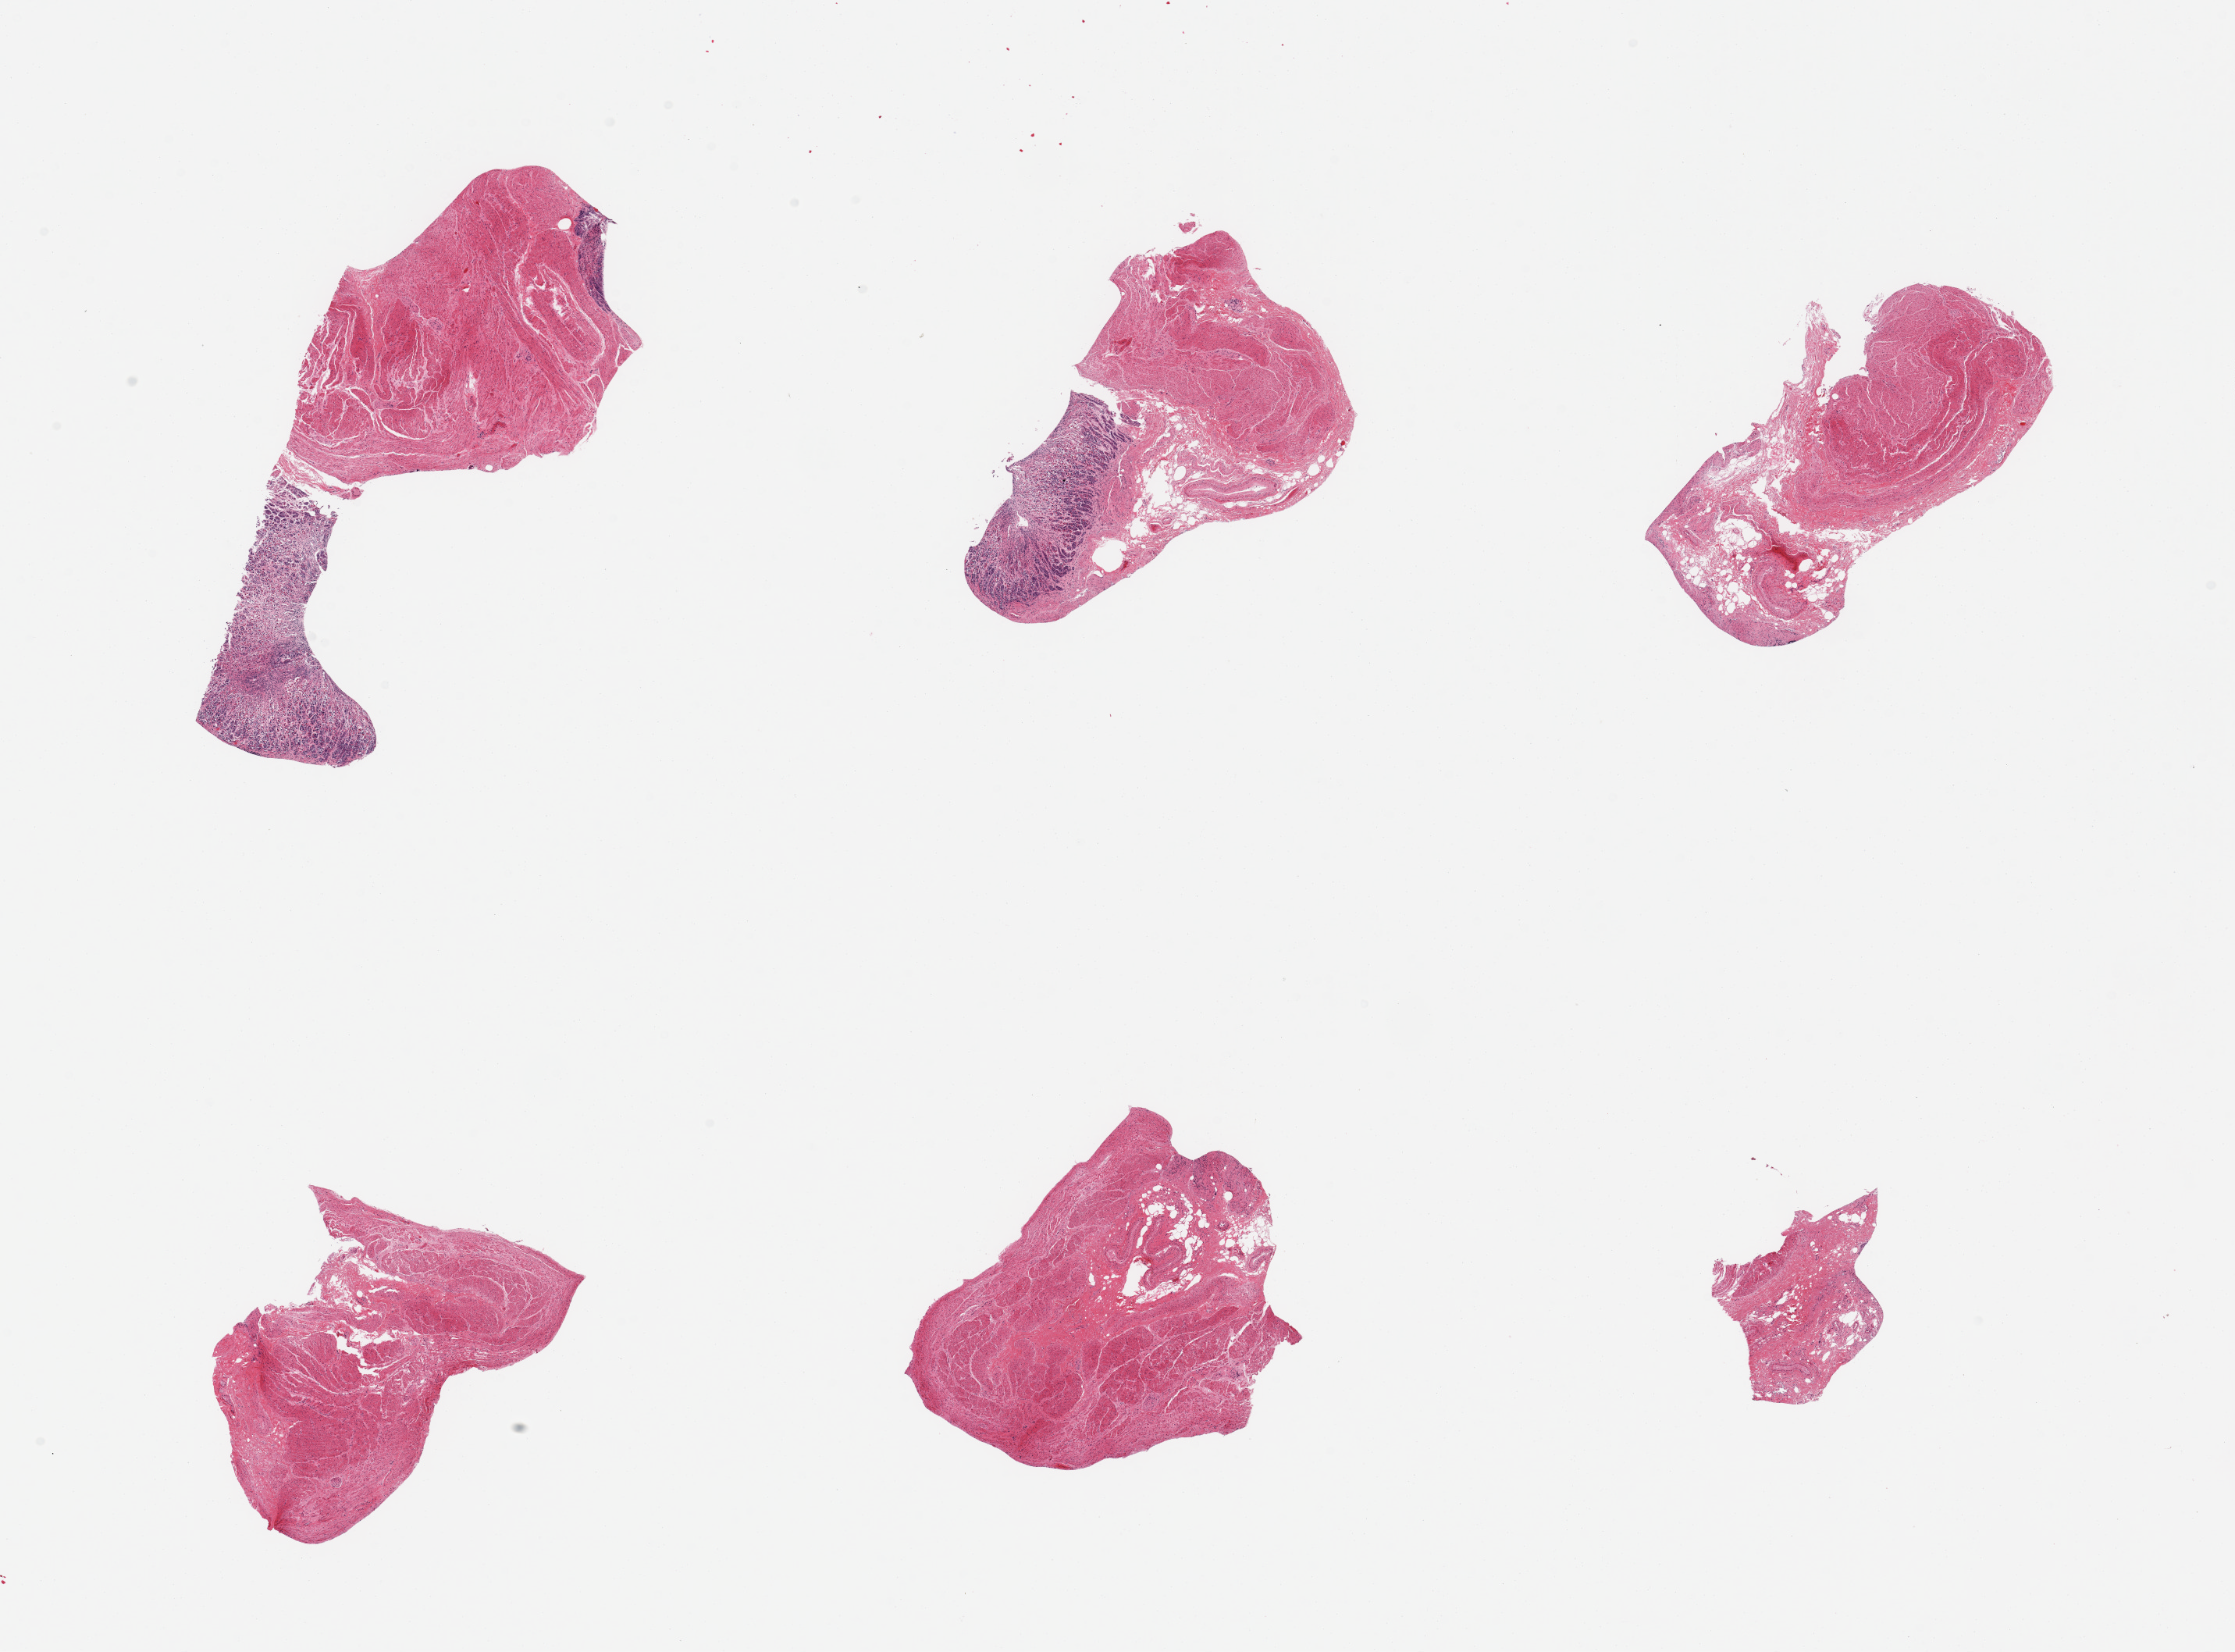
Whole-slide image, hematoxylin and eosin (H&E) stain, brightfield, shown as a low-resolution overview of the whole scanned area (about 22.6 x 16.7 mm, slide scanned at 20x). PAXgene-fixed paraffin-embedded (PFPE) section. Target tissue: stomach. Tissue donor sample. Donor sex: female.
• pathologist's review note for this sample: 6 pieces; mucosa autolyzed or absent; muscularis intact